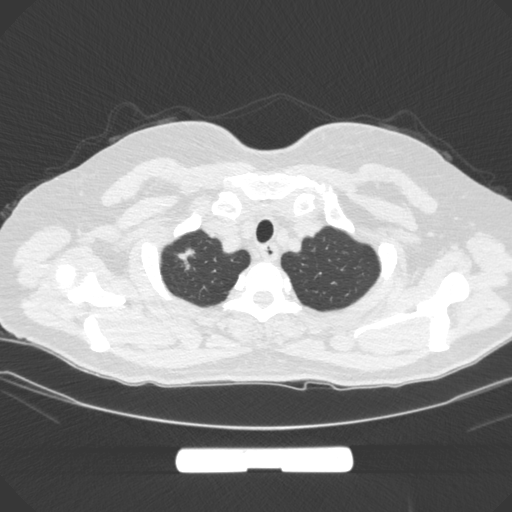
Chest CT, one axial slice. Position 264 of 295 along the scan axis. 120 kVp. Lung window (W 1500 / L -600 HU). 512 × 512 image matrix, field of view 369 × 369 mm. Patient: female, 58 years. Case-level facts recorded for this patient, not image findings: clinical TNM (as recorded): T1b N0 M0.
Annotated regions visible in this slice (bounding box drawn by a radiologist):
- lung tumour (recorded histology: adenocarcinoma): bounding box [x1, y1, x2, y2] px = [172, 239, 205, 281]